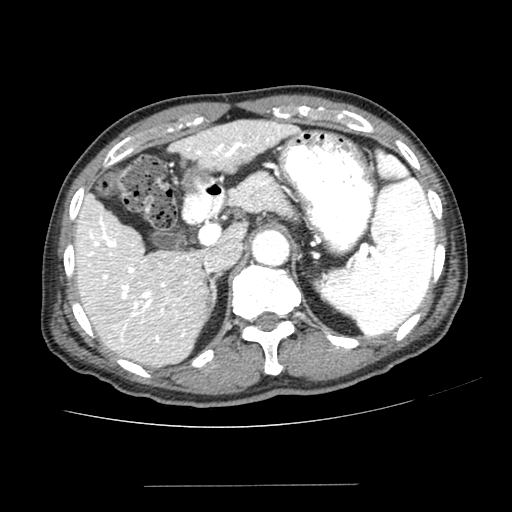
Contrast-enhanced abdominal CT (liver protocol), one axial slice. Slice 155 of 187 in the series (ordered by position). Reconstruction kernel SOFT. 100 kVp. One of 2 acquisitions stored at this slice position. Soft-tissue window (W 400 / L 40 HU). 512 × 512 image matrix. Case-level facts recorded for this patient, not image findings: diagnosis: hepatocellular carcinoma (patient treated with transarterial chemoembolisation; whether this scan precedes or follows treatment is not stated here); TNM stage (as recorded): Stage-I; Child-Pugh class: A; tumour differentiation: poorly differentiated; tumour size: 1.6 cm.
Outlined on this slice (semi-automatically segmented with operator editing):
- liver parenchyma outside the tumour (the mass and vessels are separate outlines, so this box may not span the whole liver): bounding box (x1, y1, x2, y2) in pixels: (76, 120, 297, 366)
- liver vessels: (80, 126, 280, 343)